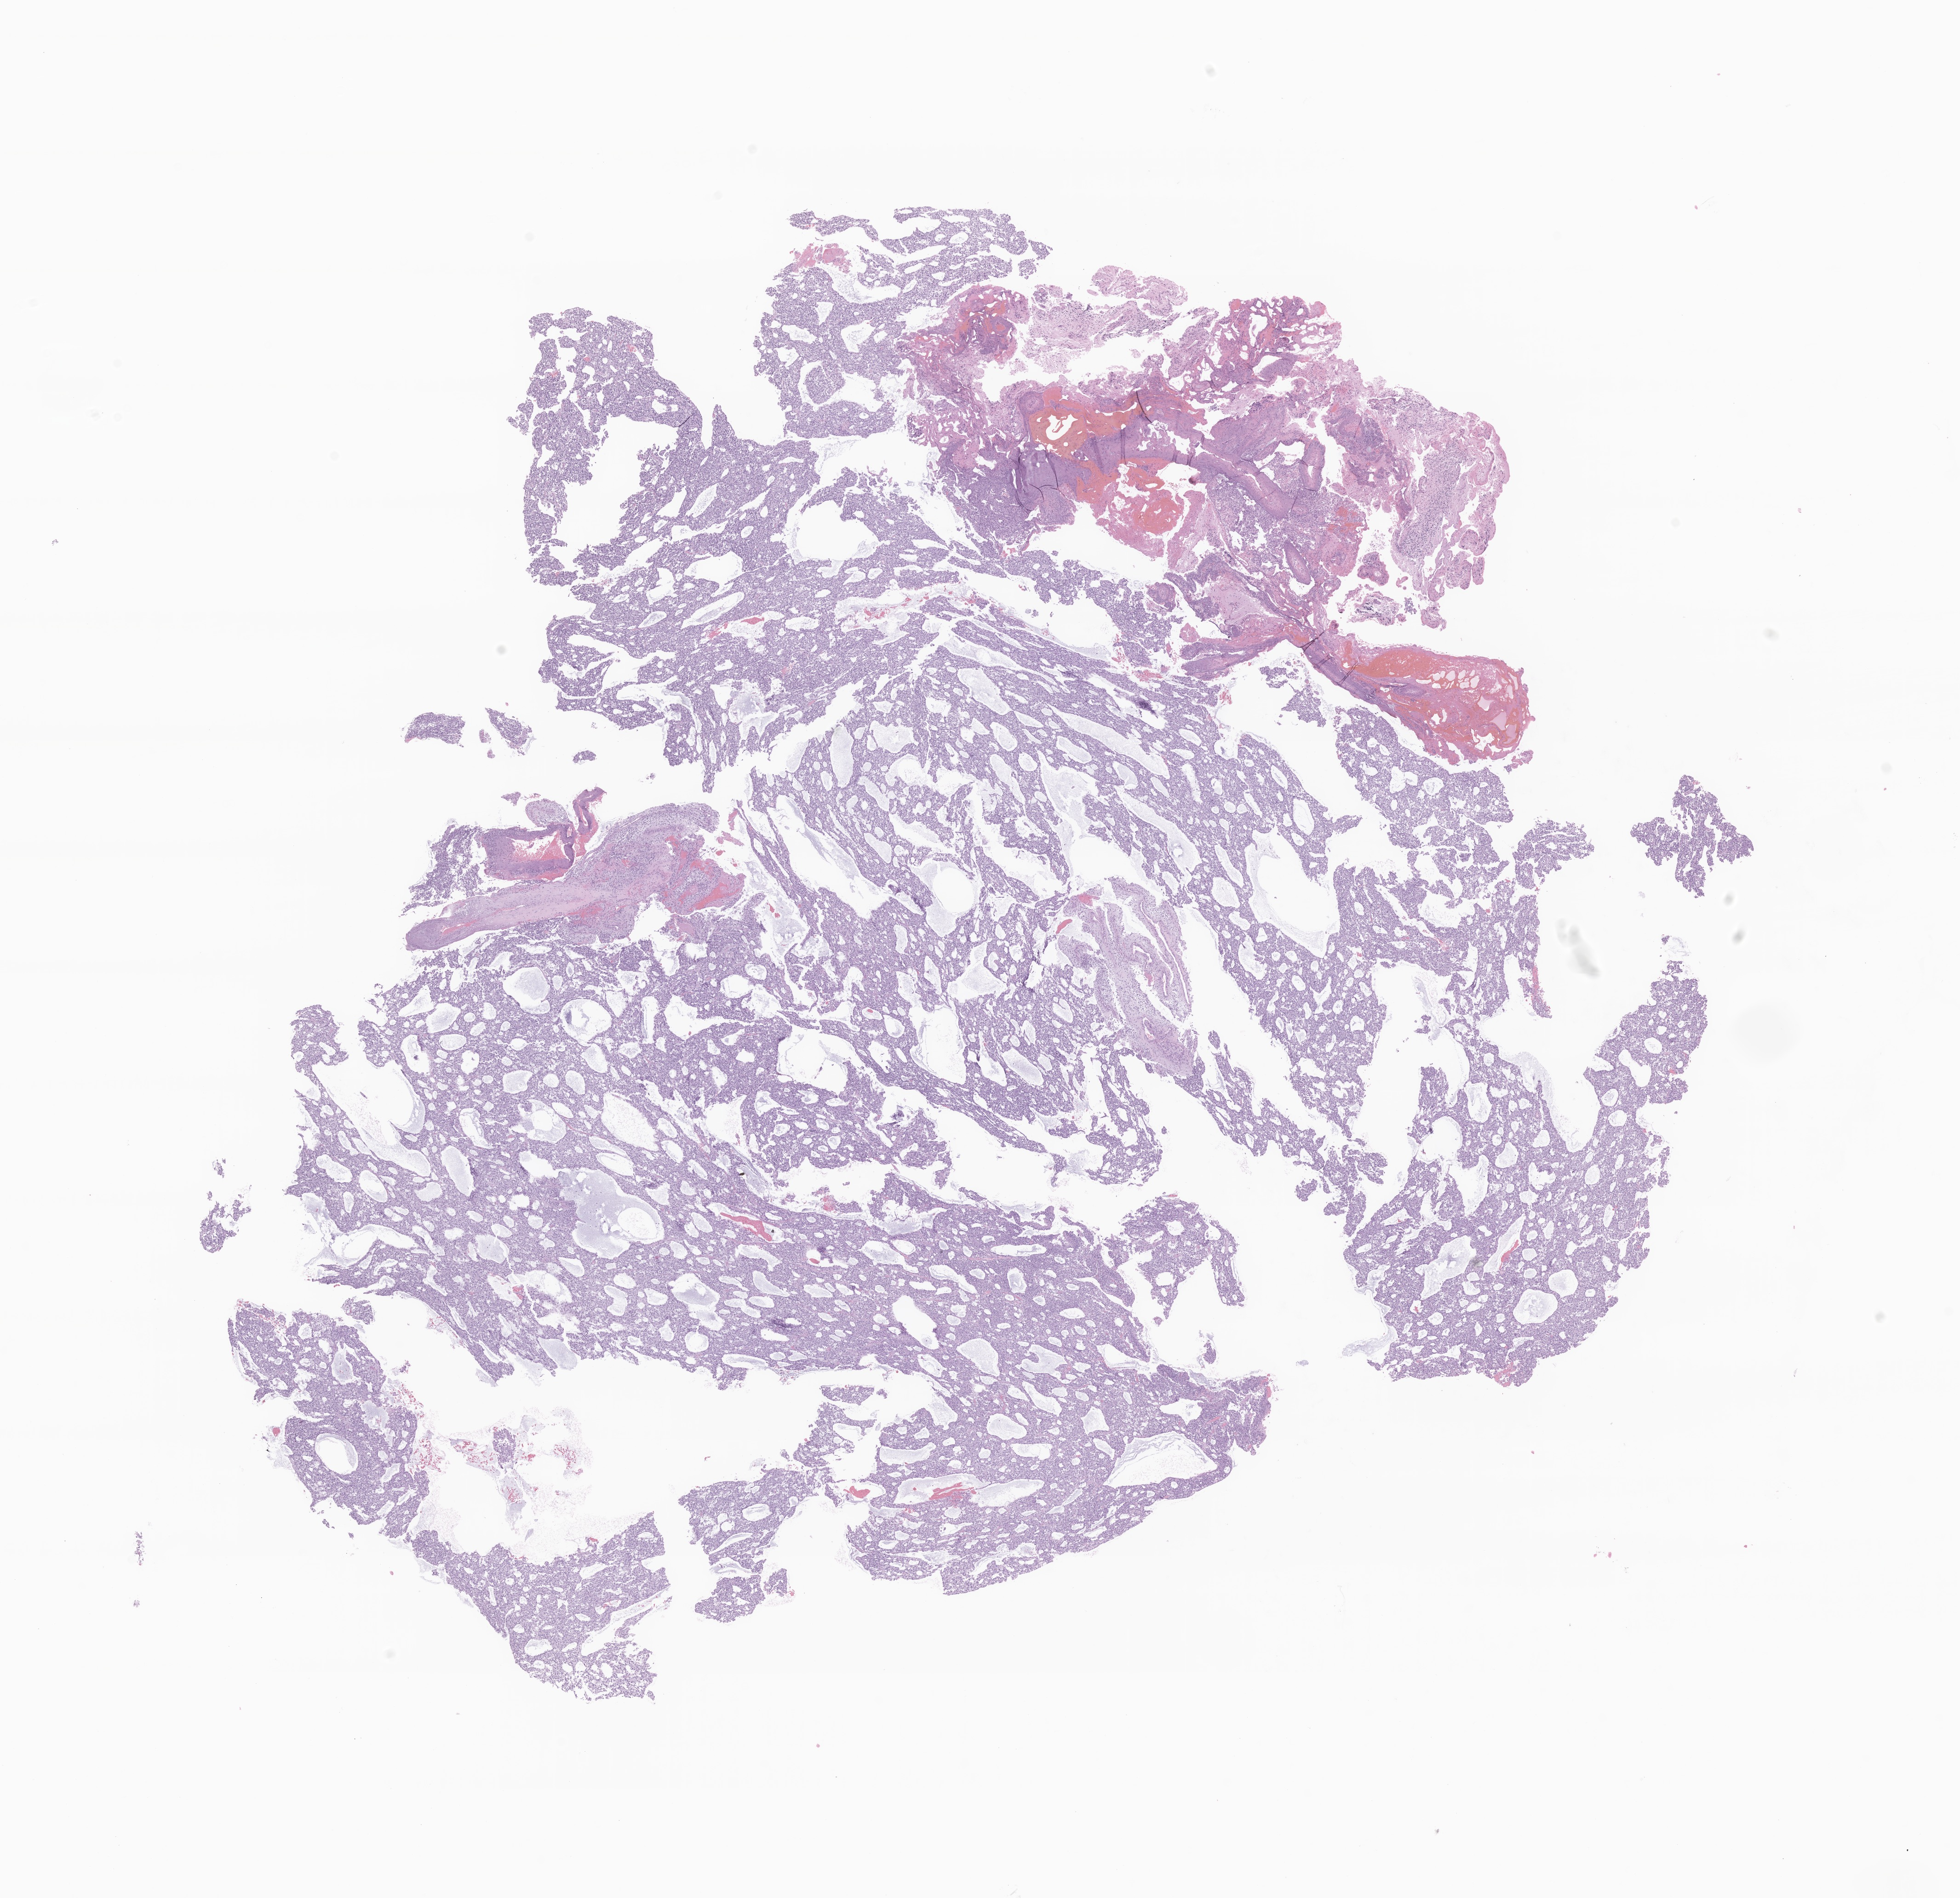
Whole-slide image, haematoxylin and eosin stain of tumor tissue from the brain — shown as a low-resolution overview of the whole scanned area (about 18.0 x 17.4 mm). FFPE section. Patient female; age 981 days (about 2.7 years).
Diagnosis: Neoplasm, uncertain whether benign or malignant.